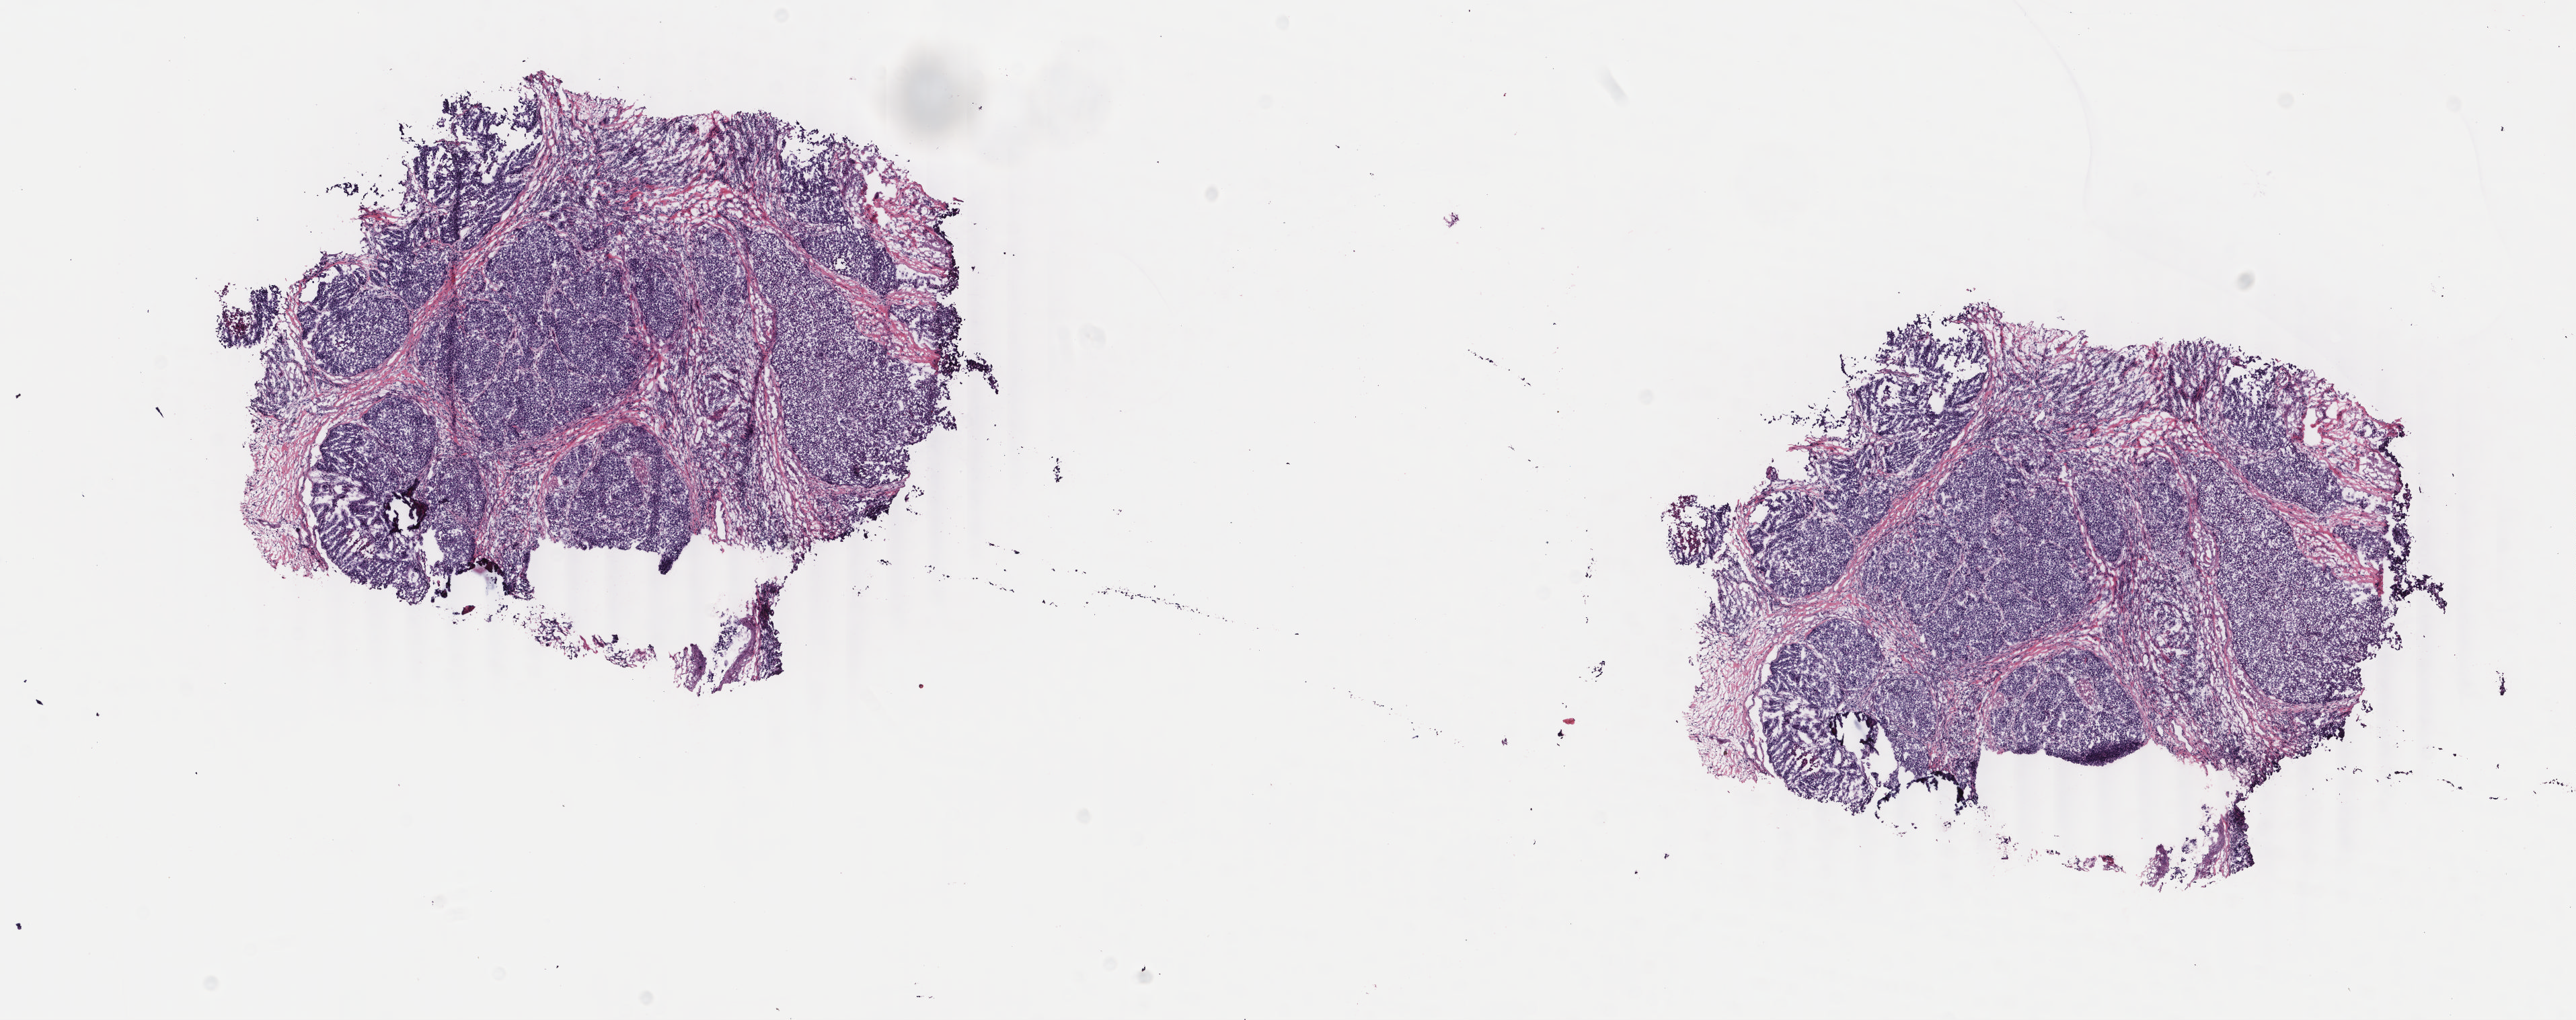
Whole-slide histology image, H&E, whole scanned area (about 15.2 x 6.0 mm, acquisition: 40x scan) shown as a low-resolution overview. Frozen section from the bottom of the tissue portion. Primary tumour sample from the breast. Female, age 66 years at initial diagnosis.
Pathologic diagnosis: Infiltrating duct carcinoma, NOS.